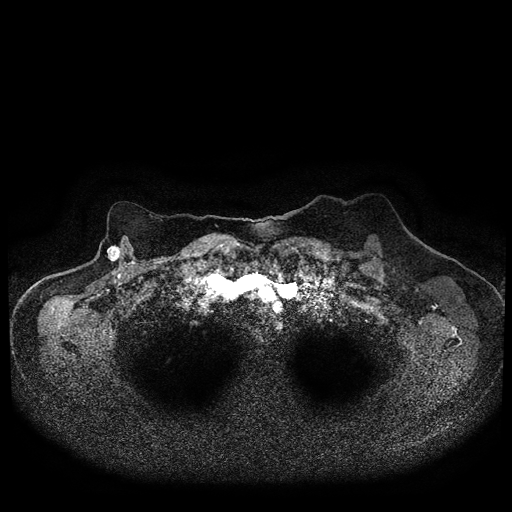
Breast MRI (dynamic contrast-enhanced, multi-phase), one axial slice; position 80 of 116 along the scan axis; dynamic contrast-enhanced series, time point 2 of 5 at this slice position (early post-contrast); 1.5 T; TE 2.7 ms, TR 5.4 ms; 2 mm slice thickness; 512 × 512 image matrix, field of view 340 × 340 mm. Female patient, age 72 years.
Structures marked on this image (semi-automatically segmented with operator editing):
- breast lesion (labelled 'tumour' in the annotation; benign lesions carry a separate 'benign' label): bounding box <105,244,122,264> (left, top, right, bottom; pixels)